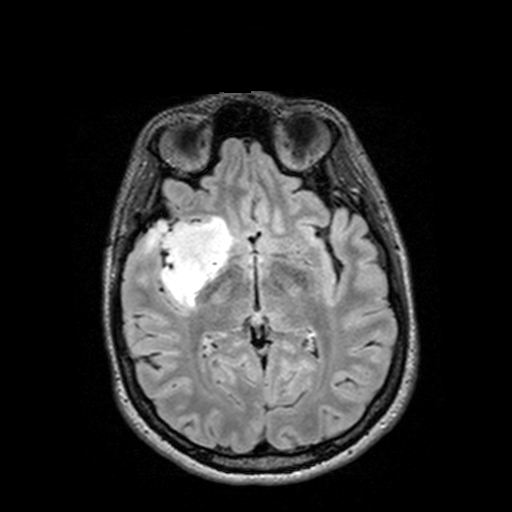
Brain MRI from a brain-tumour surgery series, one axial slice; slice 75 of 144 in the series (ordered by position); T2 FLAIR; 1 mm slice thickness; 512 × 512 image matrix, field of view 250 × 250 mm. From the clinical record (not read from this slice): histopathology: Astrocytoma; WHO grade: 3; IDH mutation: yes.
Outlined on this slice (expert manual segmentation):
- tumour: bounding box <126,217,232,305> (left, top, right, bottom; pixels)